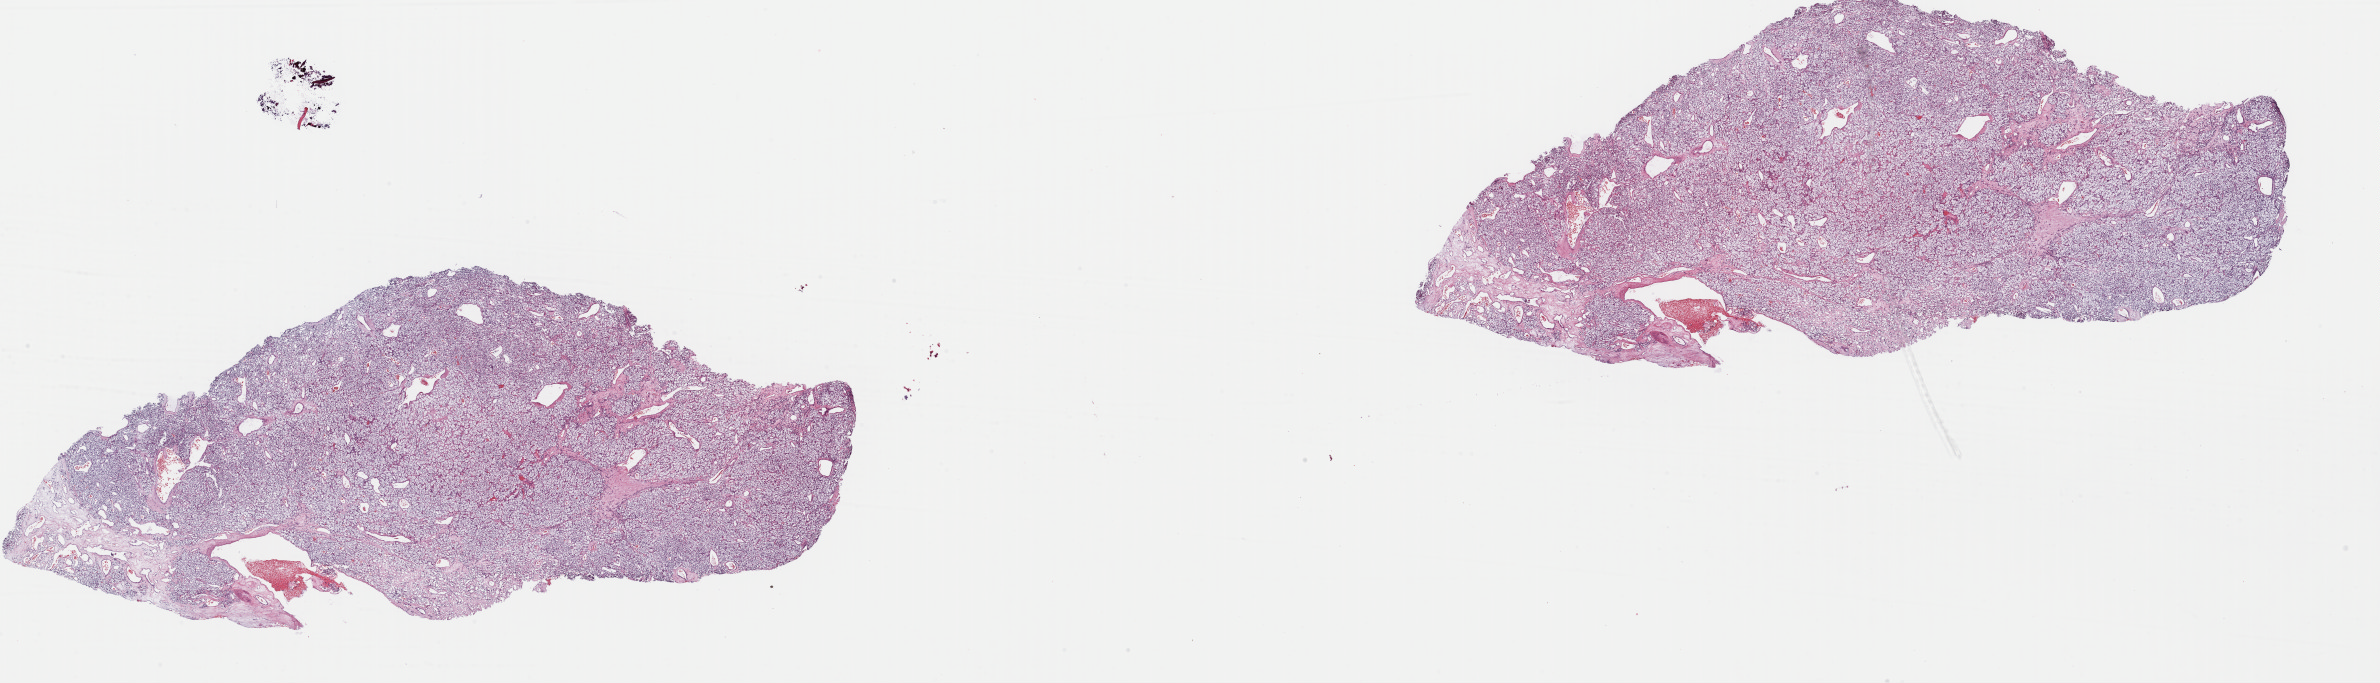
Hematoxylin and eosin (H&E) stained whole-slide image, shown as a low-resolution overview of the whole scanned area (about 37.6 x 10.8 mm, acquisition: 40x scan); formalin-fixed paraffin-embedded (FFPE) diagnostic section; sample: primary tumour, kidney. Male patient; age at initial diagnosis 61 years.
- AJCC pathologic stage: II (7th edition)
- pathologic diagnosis: Clear cell adenocarcinoma, NOS
- laterality: right